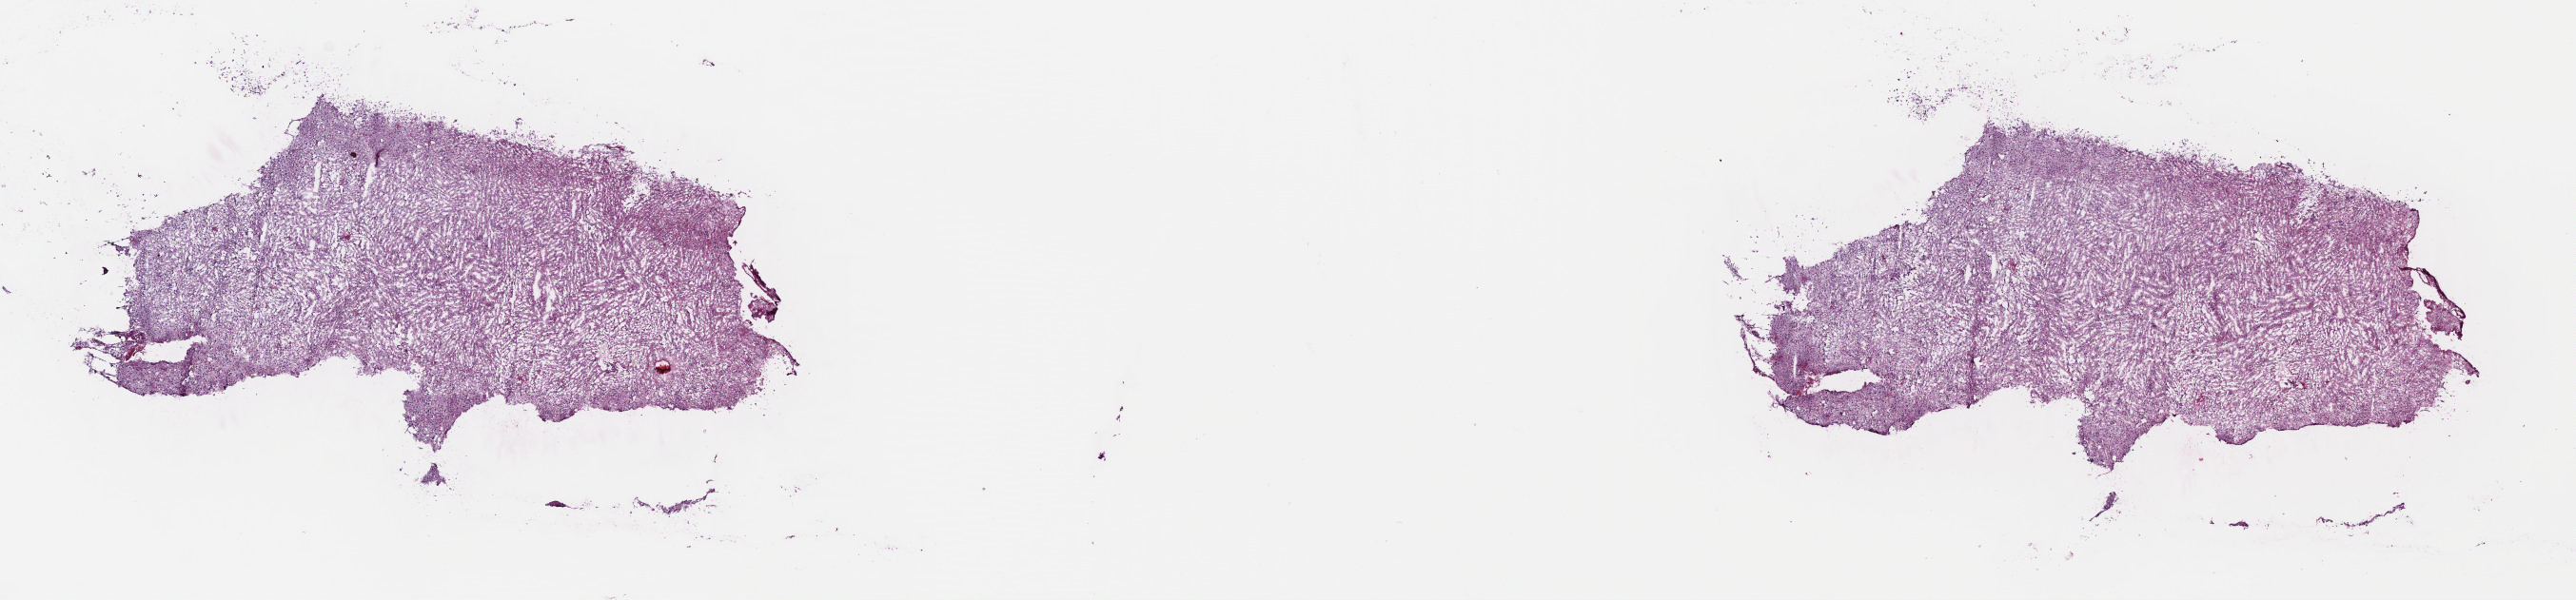
Whole-slide histology image, Hematoxylin and eosin (H&E) stained, a low-resolution overview of the entire scanned area, about 21.3 x 5.0 mm. Frozen section. Sample: primary tumour, brain. Male patient; age at initial diagnosis 26 years. Histologic grade: G3 (poorly differentiated). Pathologist review of this section (percent, as recorded): tumour cells 50%, tumour nuclei 80%, normal cells 10%, stromal cells 40%, necrosis 0%. Infiltration values recorded for this section: lymphocyte infiltration 0%, monocyte infiltration 0%, neutrophil infiltration 0%.
Laterality: left. Histologic diagnosis: Mixed glioma (cerebrum).